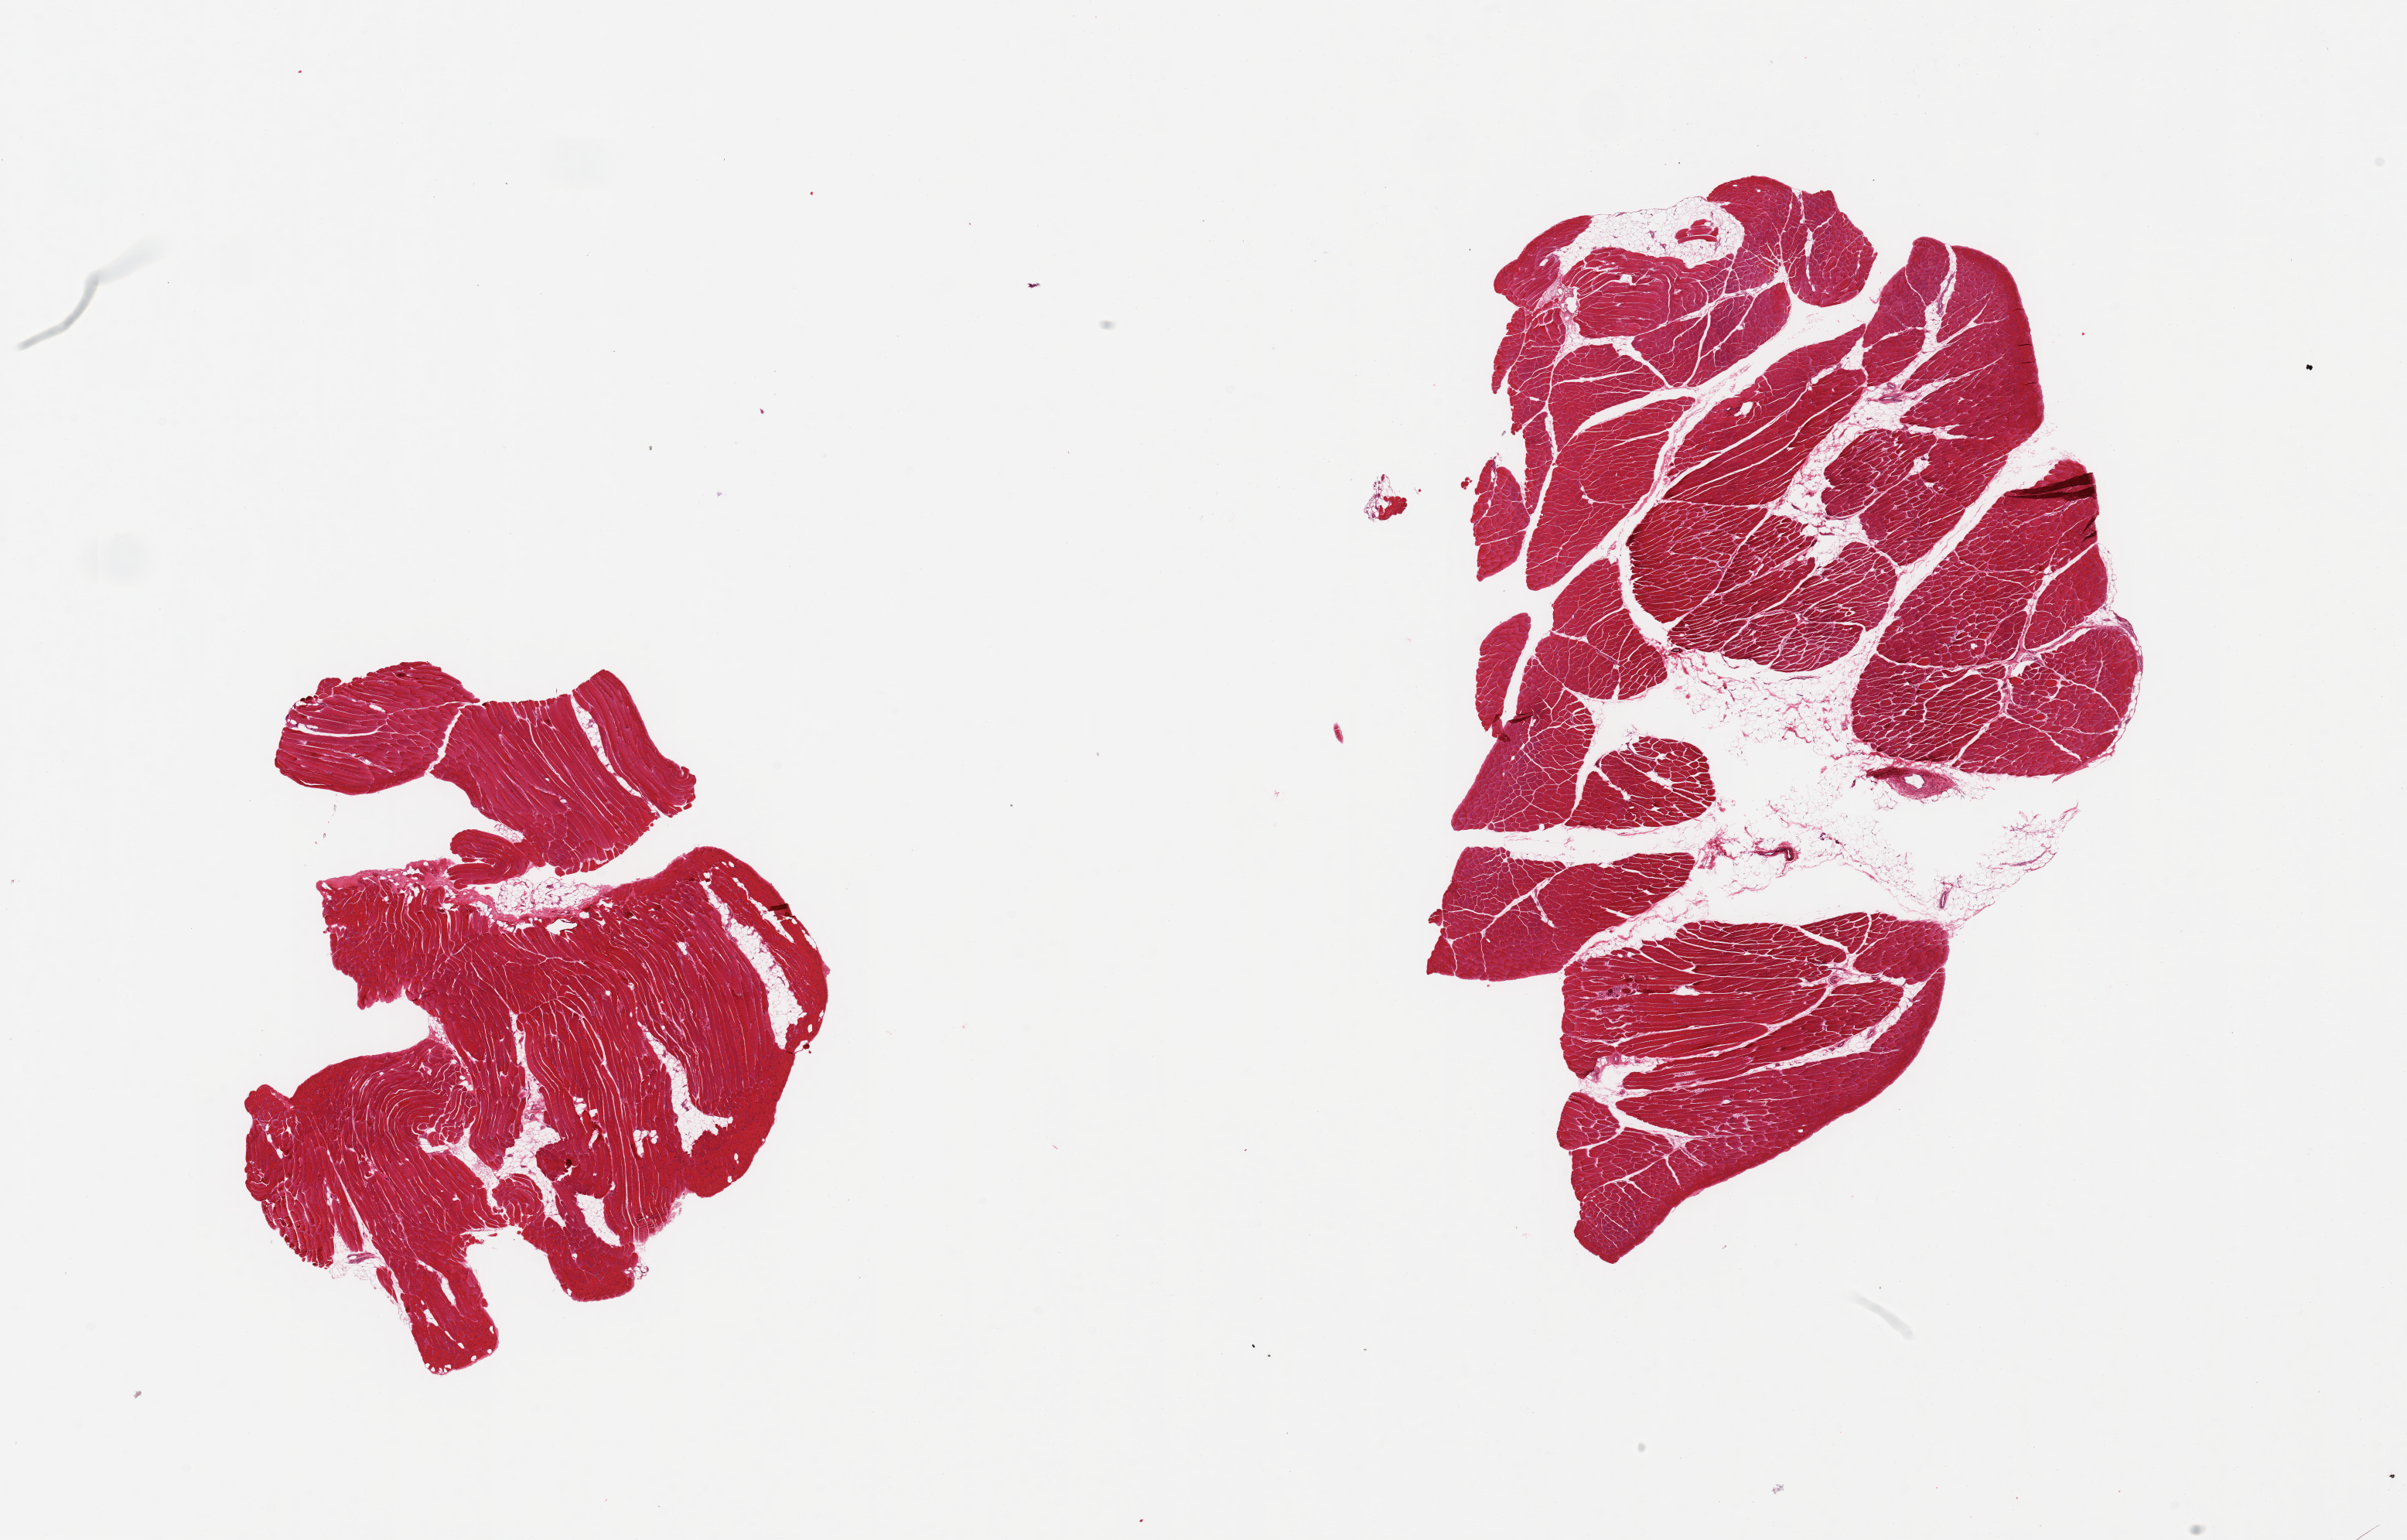
Hematoxylin and eosin (H&E) whole-slide image — low-resolution overview of the scanned area, about 24.6 x 15.7 mm (from a 20x scan). PAXgene-fixed, paraffin-embedded tissue. Sampled site (target tissue): skeletal muscle. Donor tissue sample. Donor sex: female.
Pathologist's review note for this sample: 2 pieces; 5% internal fat.